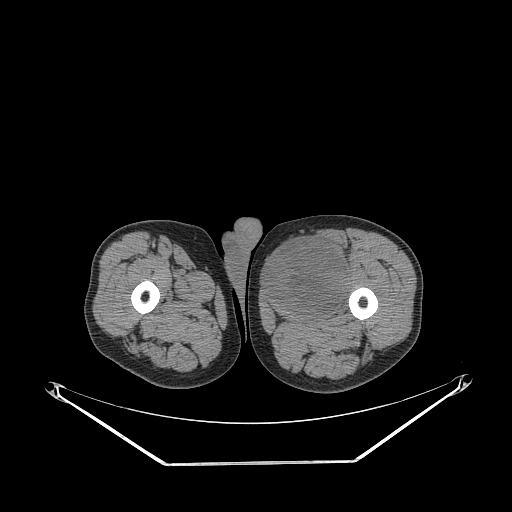
CT of an extremity soft-tissue mass (from a PET/CT study), one axial slice; position 253 of 267 along the scan axis; reconstruction kernel STANDARD; soft-tissue window (W 400 / L 40 HU); 512 × 512 image matrix, field of view 500 × 500 mm. Male patient. From the clinical record (not read from this slice): histological type: pleiomorphic liposarcoma; grade: high; site of the primary tumour: left thigh.
Structures marked on this image (expert contour drawn on MRI and transferred to this co-registered scan by the dataset authors):
- gross tumour volume including surrounding oedema: box from (x=267, y=235) to (x=353, y=312) px
- gross tumour volume (mass): (x=267, y=237)–(x=350, y=312)